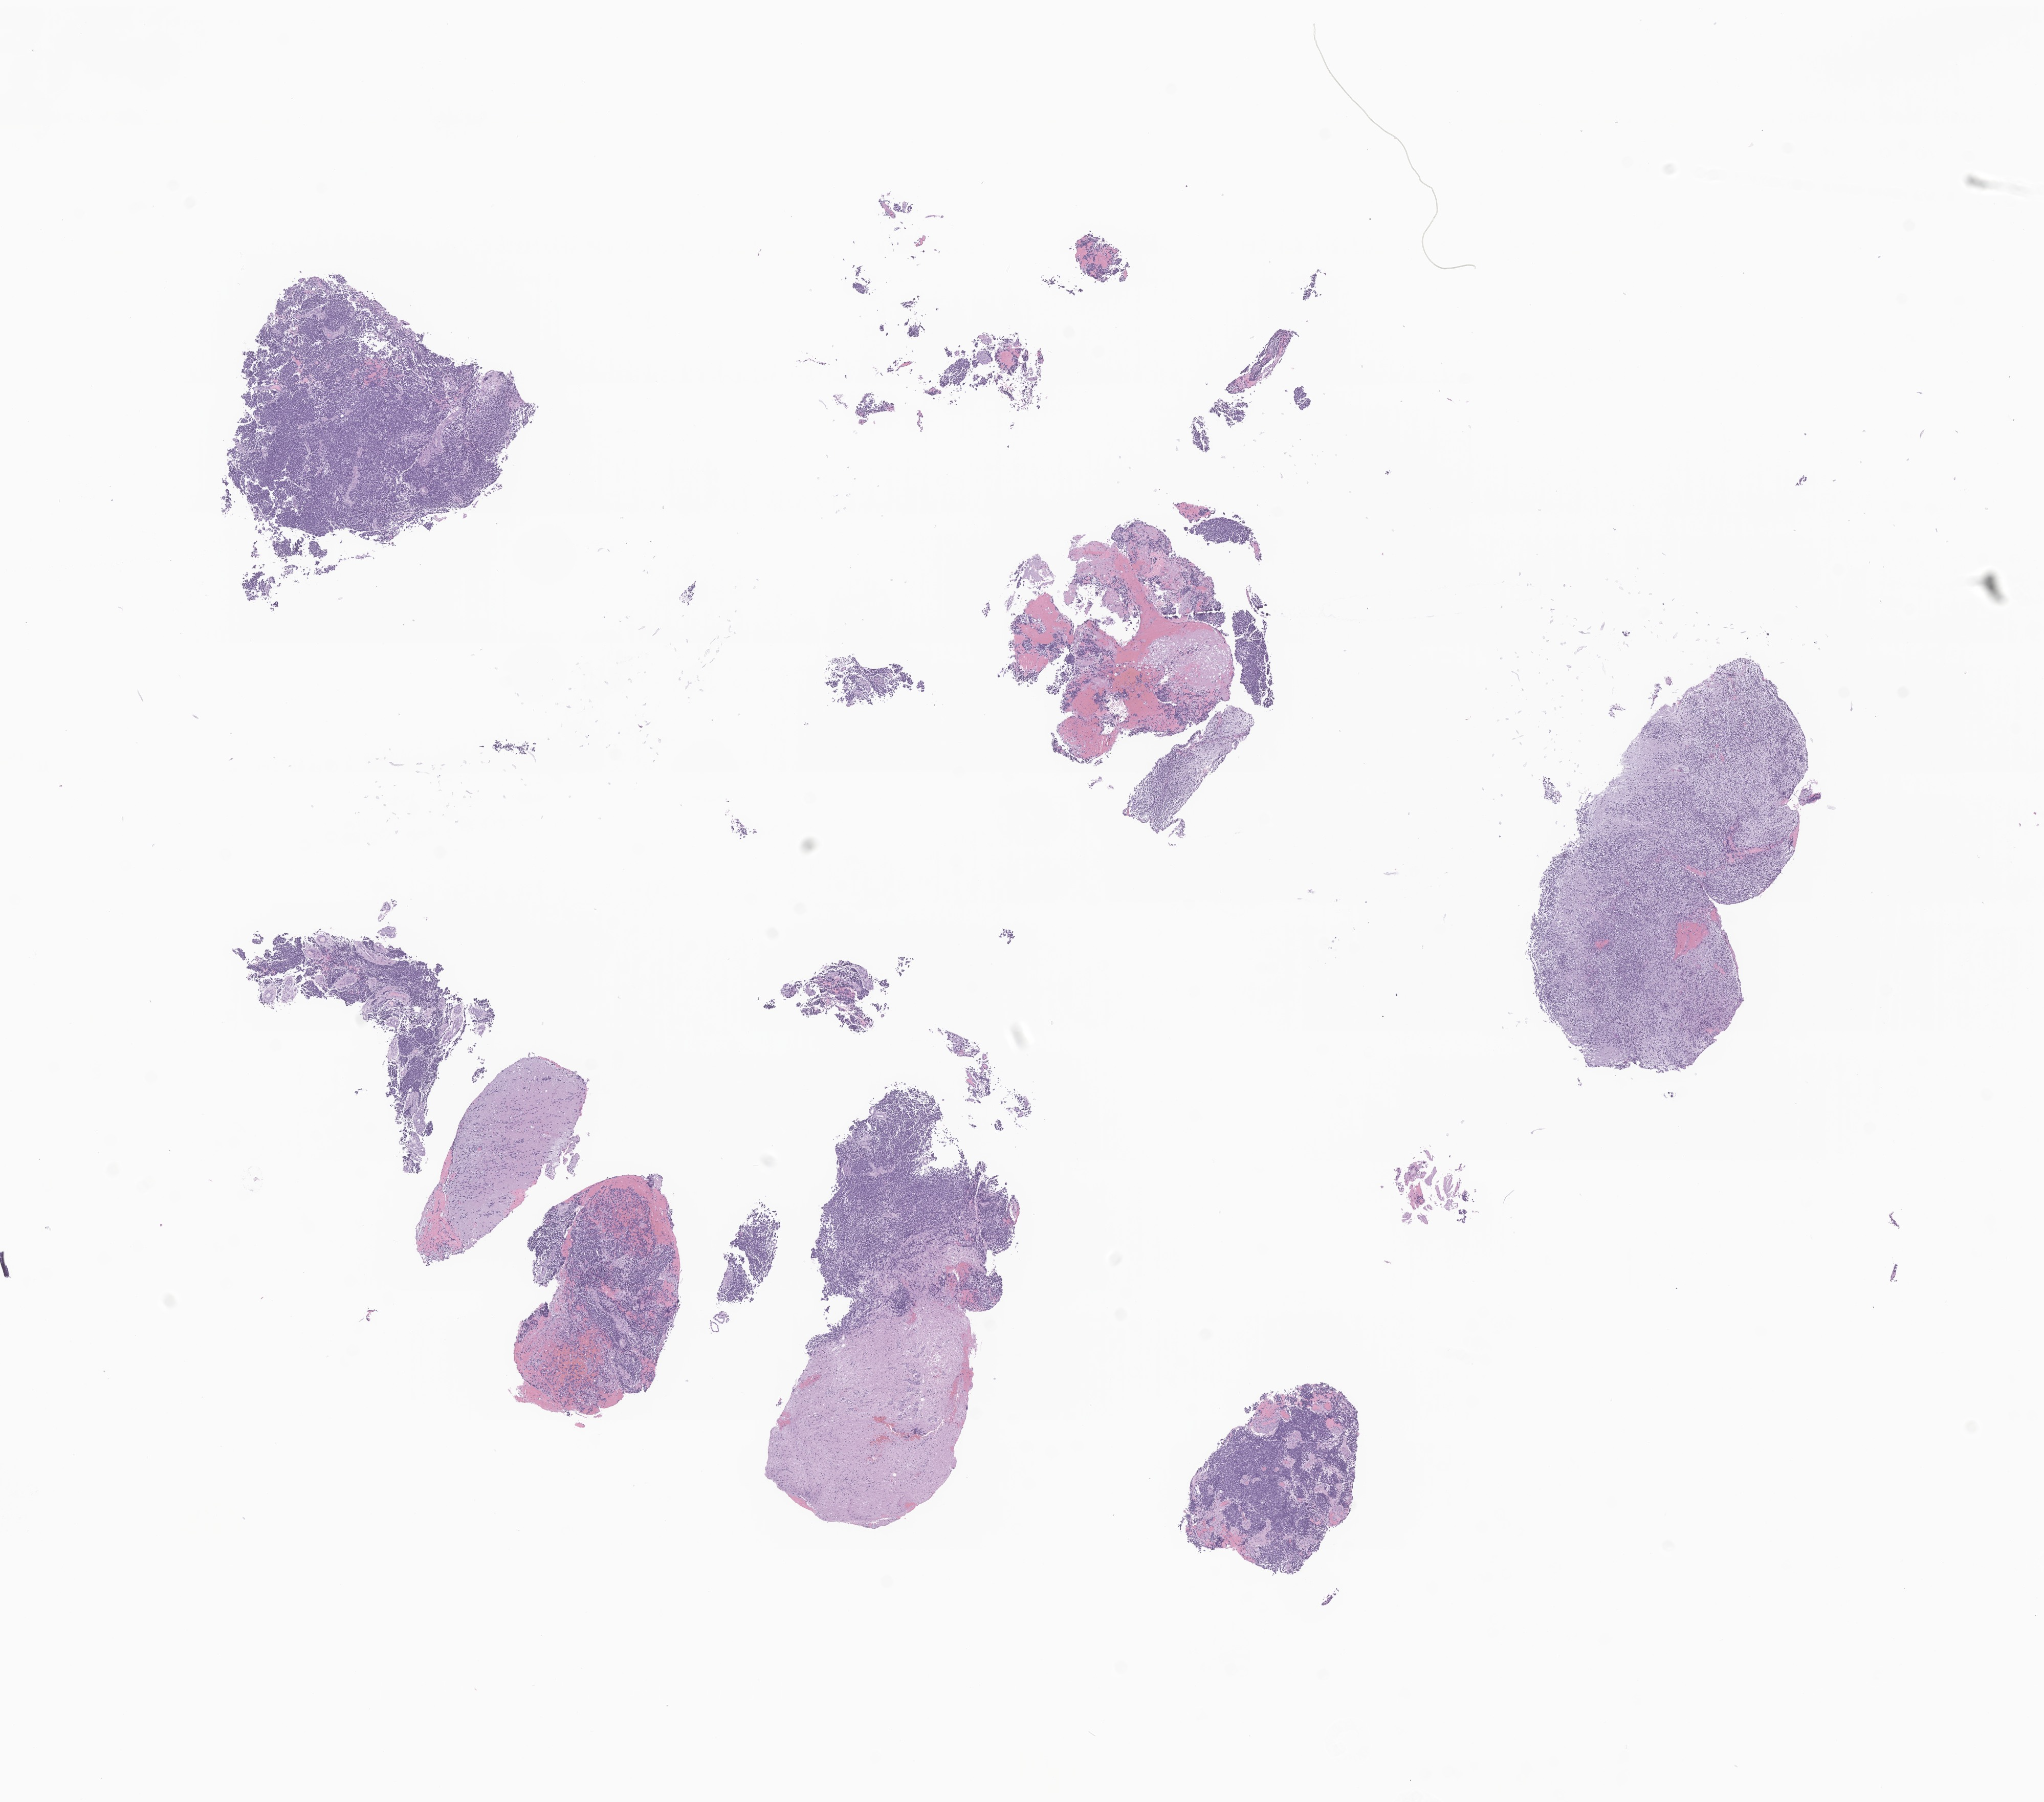
Whole-slide image, haematoxylin and eosin stain of tumor tissue from the brain, low-resolution overview of the scanned area, about 16.8 x 14.8 mm. FFPE section. Patient: male, age 122 months (10 years 2 months).
Diagnosis (ICD-O-3 morphology term): Medulloblastoma, NOS.